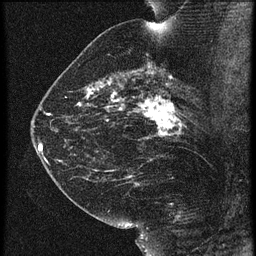
Breast MRI (dynamic contrast-enhanced), one sagittal slice; slice 37 of 60 in the series (ordered by position); 3 images stored at this slice position (order not interpretable as contrast timing); 1.5 T; TE 4.2 ms, TR 21.3 ms; 1.5 mm slice thickness; 256 × 256 image matrix, field of view 180 × 180 mm. Female patient, age 42 years. Case-level facts recorded for this patient, not image findings: setting: breast cancer imaged before/during neoadjuvant chemotherapy; receptor status: HER2-positive.
Outlined on this slice (semi-automatic segmentation, software-assisted and operator-edited):
- analysis volume of interest (the breast-tissue region the enhancement analysis was run in; not a lesion): box from (x=122, y=82) to (x=195, y=147) px
- tumour enhancement mask (voxels above the 90 % enhancement threshold inside the analysis volume of interest): (x=122, y=86)–(x=181, y=139)